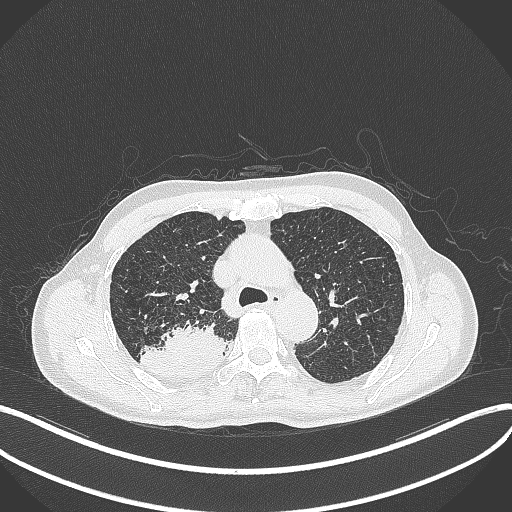
Chest CT, one axial slice. Slice 320 of 428 in the series (ordered by position). Reconstruction kernel B70f. Lung window (W 1500 / L -600 HU). 1 mm slice thickness. 512 × 512 image matrix, field of view 400 × 400 mm. Patient: male, 79 years. From the clinical record (not read from this slice): clinical TNM (as recorded): T3 N0 M0.
Outlined on this slice (bounding box drawn by a radiologist):
- lung tumour (recorded histology: adenocarcinoma): box from (x=138, y=321) to (x=227, y=382) px